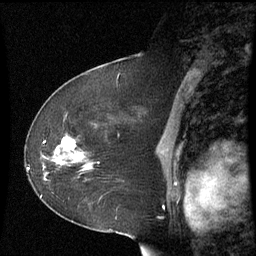
Breast MRI (dynamic contrast-enhanced), one sagittal slice. Slice 36 of 60 in the series (ordered by position). Dynamic contrast-enhanced series, image 2 of 3 at this slice position (ordered by acquisition). 1.5 T. TE 4.2 ms, TR 8.9 ms. 256 × 256 image matrix, field of view 210 × 210 mm. Female patient, age 51 years. From the clinical record (not read from this slice): setting: breast cancer imaged before/during neoadjuvant chemotherapy; receptor status: HR-positive, HER2-negative.
Annotated regions visible in this slice (semi-automatic segmentation, software-assisted and operator-edited):
- analysis volume of interest (the breast-tissue region the enhancement analysis was run in; not a lesion): bounding box (x1, y1, x2, y2) in pixels: (50, 117, 96, 174)
- tumour enhancement mask (voxels above the 70 % enhancement threshold inside the analysis volume of interest): (63, 138, 83, 157)